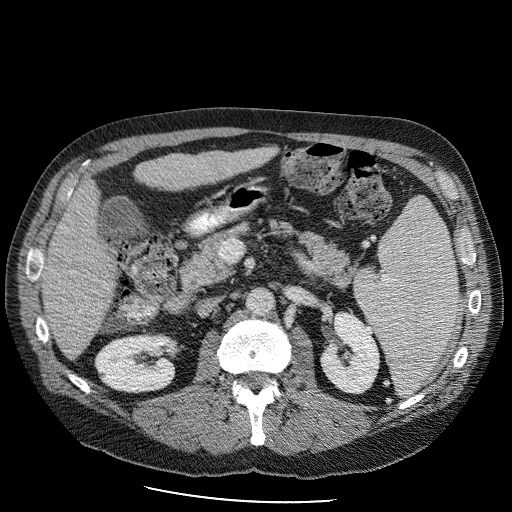
Contrast-enhanced abdominal CT (liver protocol), one axial slice; slice 36 of 98 in the series (ordered by position); soft-tissue window (W 400 / L 40 HU); 512 × 512 image matrix. From the clinical record (not read from this slice): diagnosis: hepatocellular carcinoma (patient treated with transarterial chemoembolisation; whether this scan precedes or follows treatment is not stated here); TNM stage (as recorded): Stage-II; Child-Pugh class: B; tumour differentiation: moderately differentiated; tumour nodularity: uninodular.
Structures marked on this image (semi-automatically segmented with operator editing):
- liver parenchyma outside the tumour (the mass and vessels are separate outlines, so this box may not span the whole liver): bounding box <40,140,285,354> (left, top, right, bottom; pixels)
- liver vessels: <85,297,88,300>